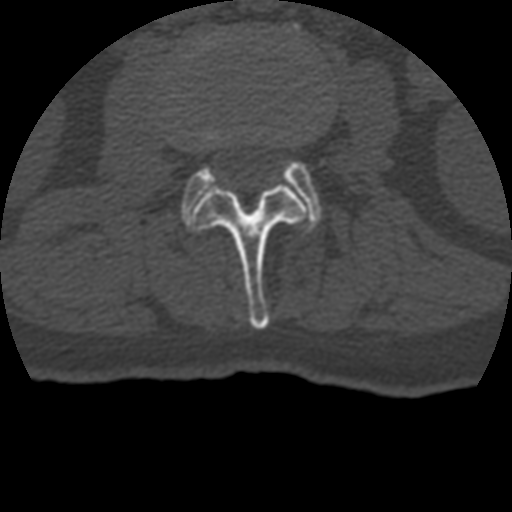
CT including the spine, one axial slice. Slice 105 of 399 in the series (ordered by position). Reconstruction kernel STANDARD. 120 kVp. Bone window (W 1800 / L 400 HU). 512 × 512 image matrix. Patient age 69 years. Case-level facts recorded for this patient, not image findings: primary cancer: prostate.
Structures marked on this image (semi-automatic segmentation, software-assisted and operator-edited):
- L2 vertebra: bounding box [x1, y1, x2, y2] px = [194, 185, 305, 329]
- L3 vertebra: [181, 32, 322, 221]